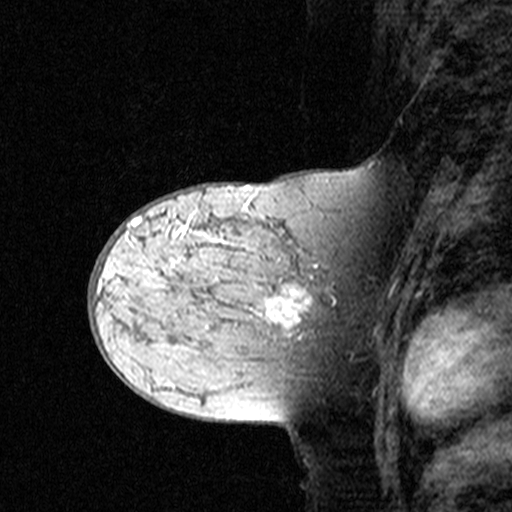
Breast MRI (dynamic contrast-enhanced), one sagittal slice. Slice 20 of 44 in the series (ordered by position). Dynamic contrast-enhanced study with each time point stored as its own series, time point 2 of 3 at this slice position (early post-contrast, ordered by acquisition time). 1.5 T. TE 4.5 ms, TR 11 ms. 512 × 512 image matrix, field of view 200 × 200 mm. Patient: female, 44 years. Case-level facts recorded for this patient, not image findings: setting: breast cancer imaged before/during neoadjuvant chemotherapy; receptor status: triple-negative.
Annotated regions visible in this slice (semi-automatic segmentation, software-assisted and operator-edited):
- analysis volume of interest (the breast-tissue region the enhancement analysis was run in; not a lesion): bounding box (x1, y1, x2, y2) in pixels: (142, 208, 349, 363)
- tumour enhancement mask (voxels above the 90 % enhancement threshold inside the analysis volume of interest): (142, 218, 334, 336)